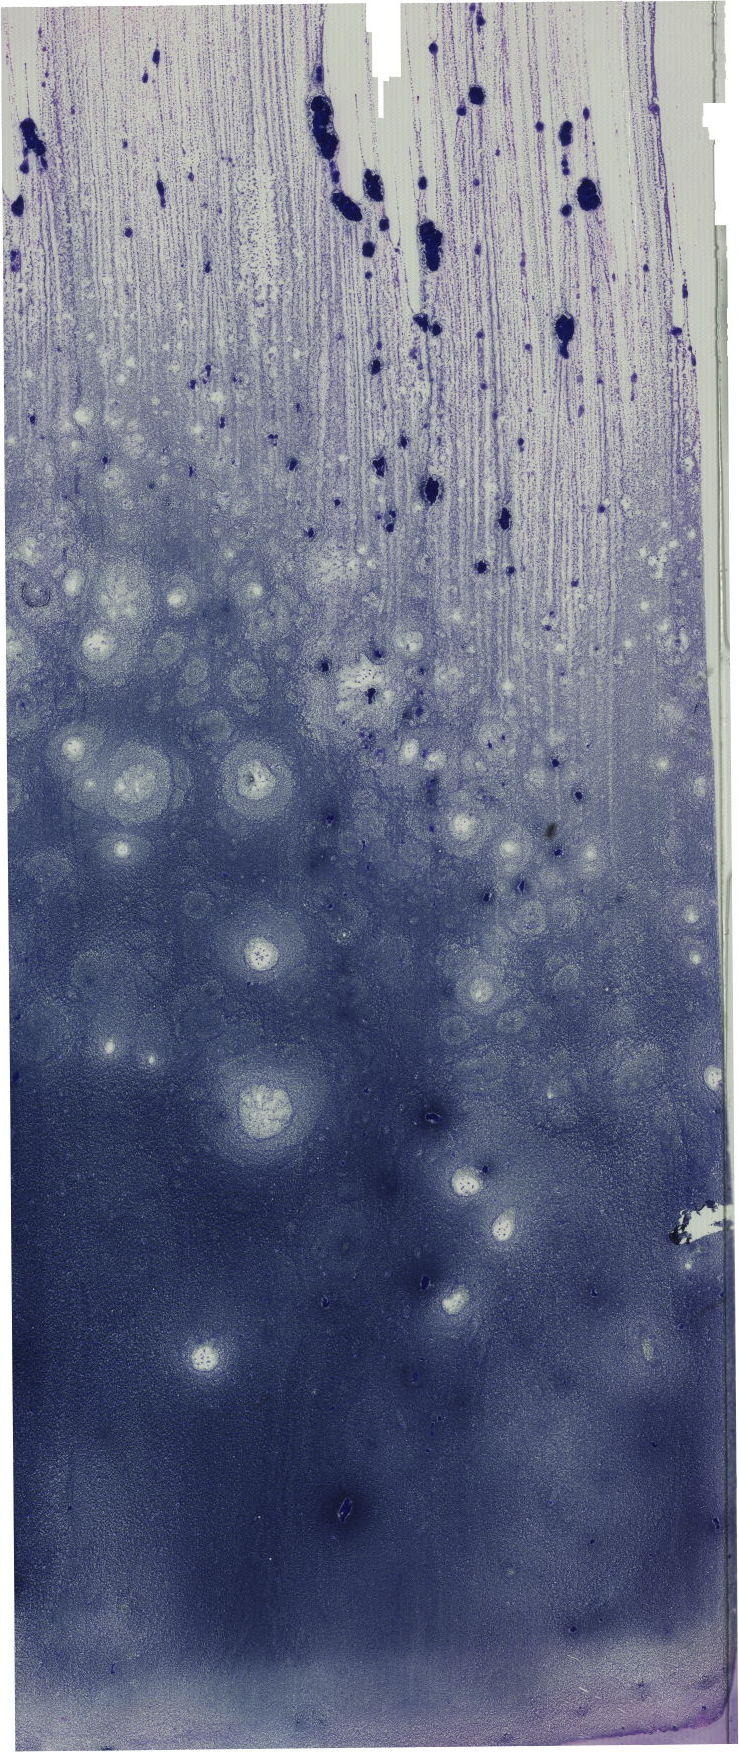
May-Grünwald–Giemsa-stained marrow aspirate smear (whole slide), a low-resolution overview of the entire scanned area, about 20.9 x 49.7 mm. Patient sex: male.
Diagnosis: B Acute Lymphoblastic Leukemia.